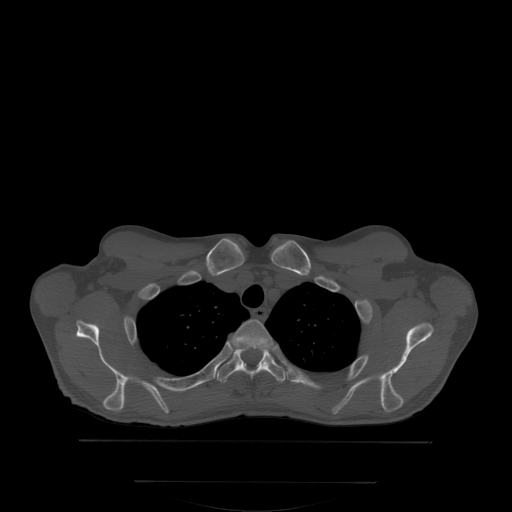
CT including the spine, one axial slice; bone window (W 1800 / L 400 HU); 2.5 mm slice thickness; 512 × 512 image matrix, field of view 500 × 500 mm. Patient: male, 58 years. From the clinical record (not read from this slice): primary cancer: prostate; vertebrae with lytic lesions (as recorded): L1.
Annotated regions visible in this slice (semi-automatically segmented with operator editing):
- T2 vertebra: box from (x=209, y=319) to (x=273, y=365) px
- T3 vertebra: (x=216, y=341)–(x=286, y=382)